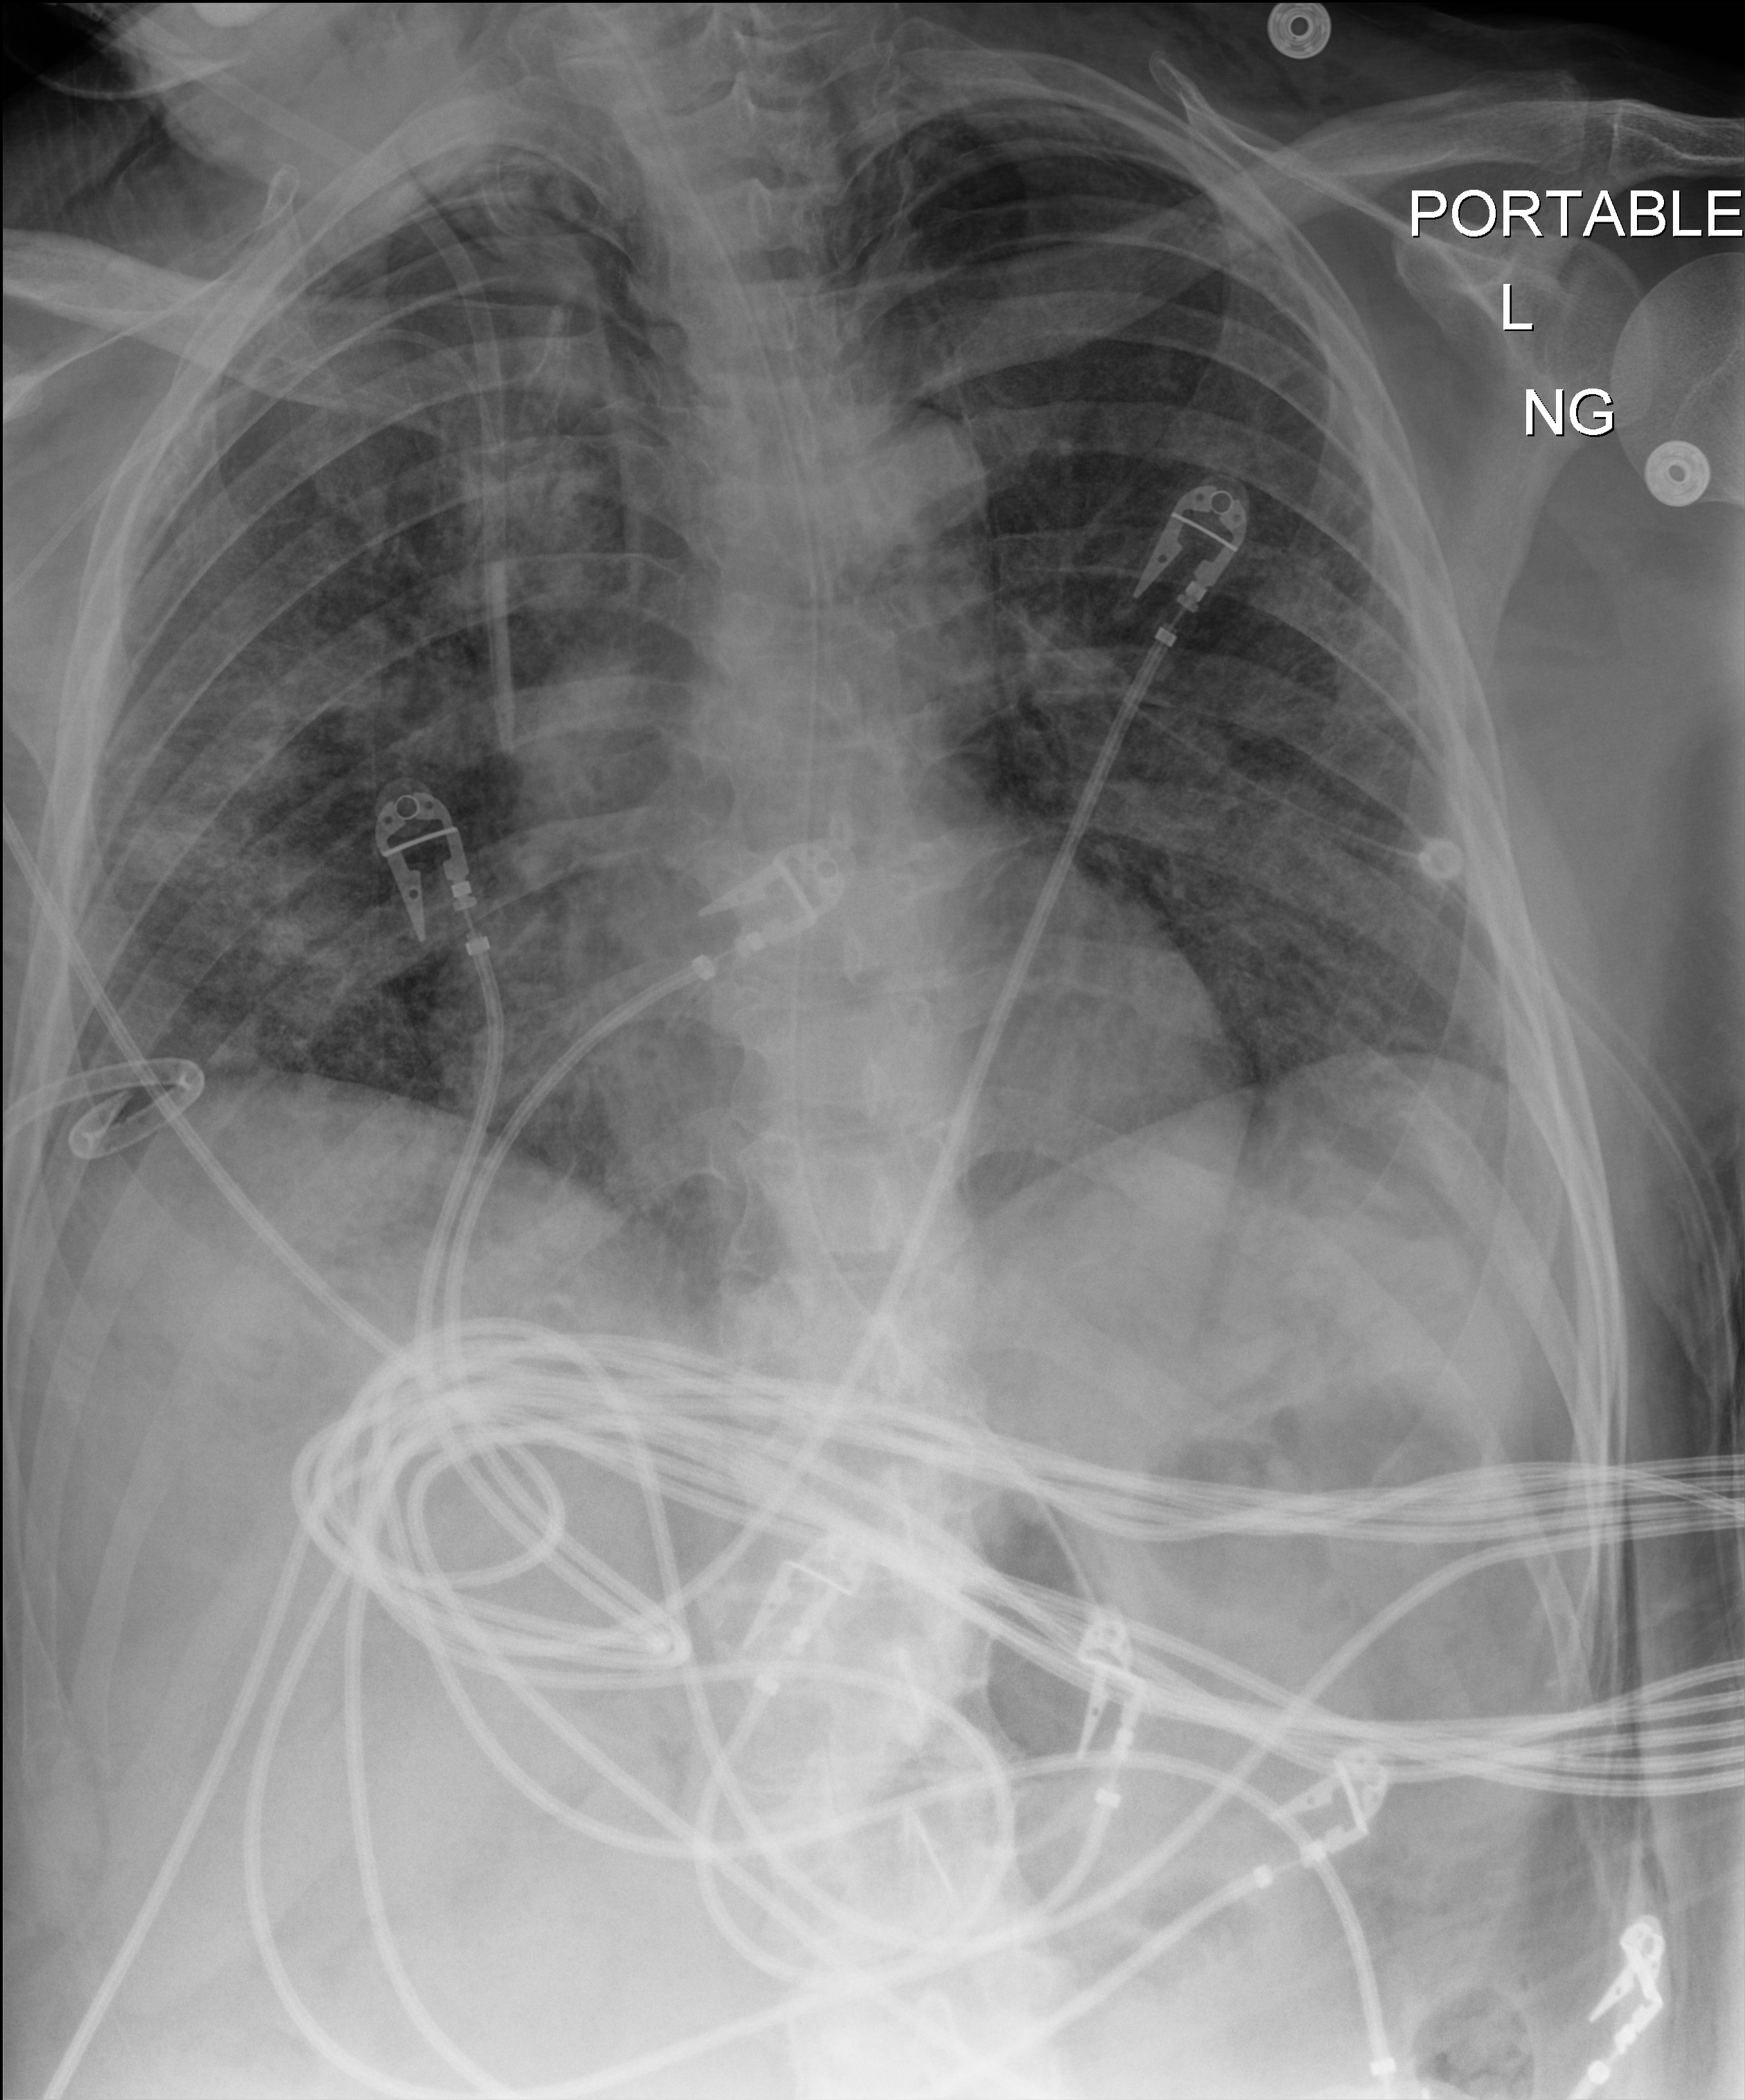
Chest X-ray (portable), anteroposterior (AP) projection. Patient hospitalised with COVID-19; male, aged 18–59 years.
Admission-level facts for this patient (not findings on this image; timing relative to this image not recorded): length of hospital stay: 77 days; admitted to intensive care during this hospital stay: yes; mechanically ventilated during this hospital stay: yes.